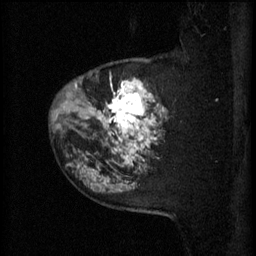
Breast MRI (dynamic contrast-enhanced), one sagittal slice; position 49 of 60 along the scan axis; 3 images stored at this slice position (order not interpretable as contrast timing); 1.5 T; TE 4.2 ms, TR 11 ms; 256 × 256 image matrix. Female patient, age 52 years.
Structures marked on this image (semi-automatically segmented with operator editing):
- analysis volume of interest (the breast-tissue region the enhancement analysis was run in; not a lesion): box from (x=81, y=58) to (x=168, y=157) px
- tumour enhancement mask (voxels above the 70 % enhancement threshold inside the analysis volume of interest): (x=81, y=78)–(x=166, y=157)